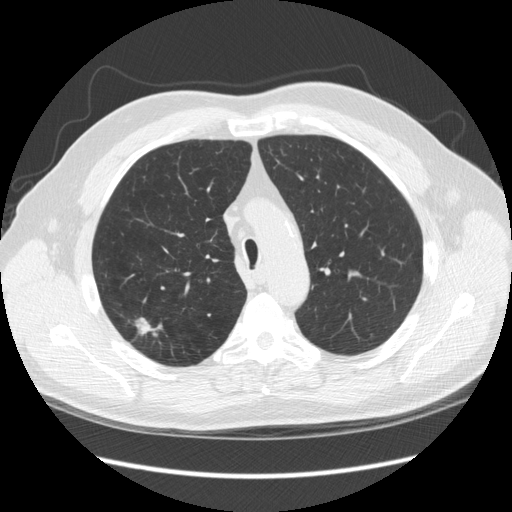
Low-dose screening chest CT, one axial slice; position 184 of 248 along the scan axis; lung window (W 1500 / L -600 HU); 2.5 mm slice thickness; 512 × 512 image matrix.
Annotated regions visible in this slice (outlined manually by an expert reader):
- lesion 1 (tumor, upper lobe of right lung): box from (x=136, y=317) to (x=152, y=335) px